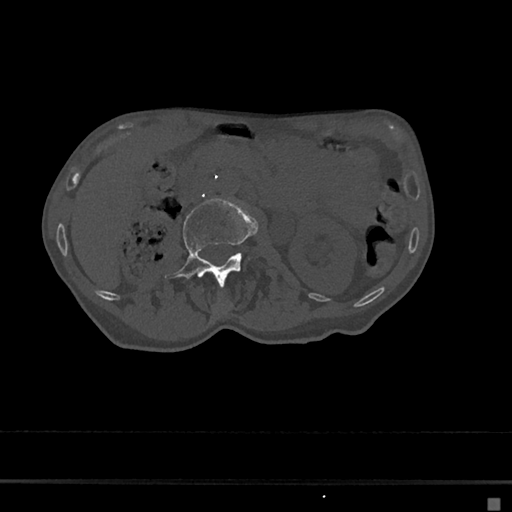
CT including the spine, one axial slice. Slice 13 of 797 in the series (ordered by position). 120 kVp. Bone window (W 1800 / L 400 HU). 512 × 512 image matrix. Female patient, age 68 years. Case-level facts recorded for this patient, not image findings: primary cancer: renal.
Outlined on this slice (semi-automatic segmentation, software-assisted and operator-edited):
- L1 vertebra: bounding box [x1, y1, x2, y2] px = [220, 299, 228, 309]
- L2 vertebra: [164, 199, 257, 283]